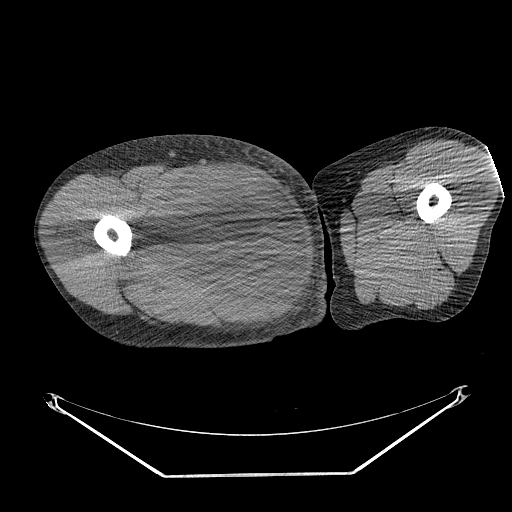
CT of an extremity soft-tissue mass (from a PET/CT study), one axial slice. Position 257 of 311 along the scan axis. Reconstruction kernel STANDARD. 140 kVp. Soft-tissue window (W 400 / L 40 HU). 512 × 512 image matrix. Male patient. From the clinical record (not read from this slice): histological type: undifferentiated - pleiomorphic; grade: high; site of the primary tumour: right thigh.
Outlined on this slice (expert contour drawn on MRI and transferred to this co-registered scan by the dataset authors):
- gross tumour volume including surrounding oedema: bounding box (x1, y1, x2, y2) in pixels: (139, 169, 266, 277)
- gross tumour volume (mass): (153, 169, 266, 271)